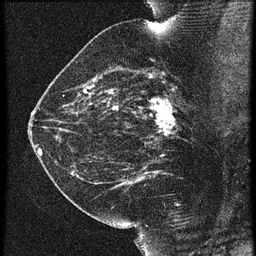
Breast MRI (dynamic contrast-enhanced), one sagittal slice; position 35 of 60 along the scan axis; 3 images stored at this slice position (order not interpretable as contrast timing); 1.5 T; TE 4.2 ms, TR 21.3 ms; 1.5 mm slice thickness; 256 × 256 image matrix, field of view 180 × 180 mm. Patient: female, 42 years. From the clinical record (not read from this slice): setting: breast cancer imaged before/during neoadjuvant chemotherapy; receptor status: HER2-positive.
Annotated regions visible in this slice (semi-automatically segmented with operator editing):
- analysis volume of interest (the breast-tissue region the enhancement analysis was run in; not a lesion): bounding box <122,82,195,147> (left, top, right, bottom; pixels)
- tumour enhancement mask (voxels above the 90 % enhancement threshold inside the analysis volume of interest): <150,98,175,133>